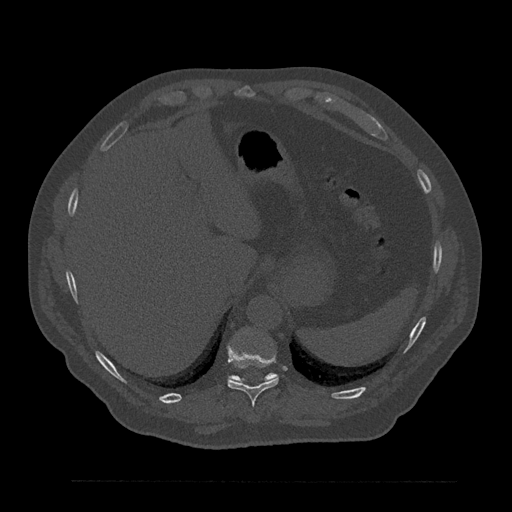
CT including the spine, one axial slice; slice 334 of 797 in the series (ordered by position); reconstruction kernel Br40s/3; bone window (W 1800 / L 400 HU); 0.5 mm slice thickness; 512 × 512 image matrix. Male patient, age 61 years. Case-level facts recorded for this patient, not image findings: primary cancer: prostate.
Annotated regions visible in this slice (semi-automatic segmentation, software-assisted and operator-edited):
- T10 vertebra: bounding box <227,343,279,407> (left, top, right, bottom; pixels)
- T11 vertebra: <228,373,278,382>